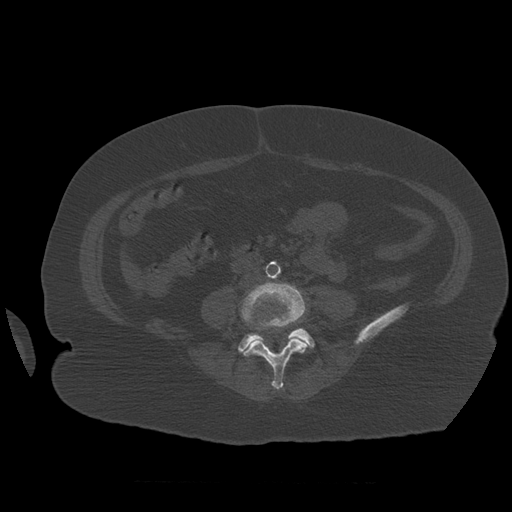
CT including the spine, one axial slice. Bone window (W 1800 / L 400 HU). 1.25 mm slice thickness. 512 × 512 image matrix, field of view 404 × 404 mm. Patient age 81 years. Case-level facts recorded for this patient, not image findings: primary cancer: renal; vertebrae with lytic lesions (as recorded): L1.
Structures marked on this image (semi-automatically segmented with operator editing):
- L4 vertebra: bounding box <241,282,310,390> (left, top, right, bottom; pixels)
- L5 vertebra: <238,328,315,355>